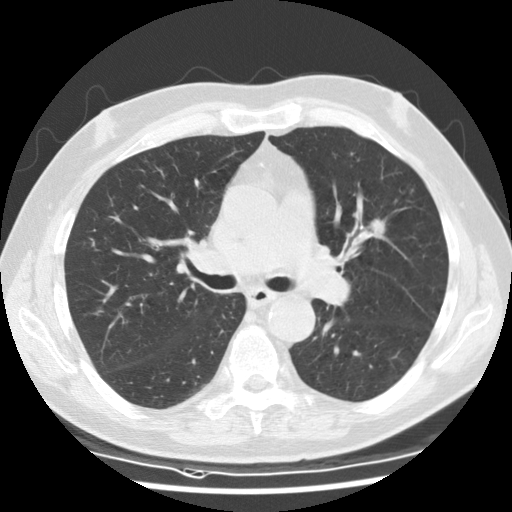
Low-dose screening chest CT, one axial slice; position 76 of 135 along the scan axis; reconstruction kernel STANDARD; 120 kVp; lung window (W 1500 / L -600 HU); 2.5 mm slice thickness; 512 × 512 image matrix, field of view 340 × 340 mm.
Outlined on this slice (outlined manually by an expert reader):
- lesion 1 (tumor, upper lobe of left lung): bounding box [x1, y1, x2, y2] px = [370, 219, 386, 234]